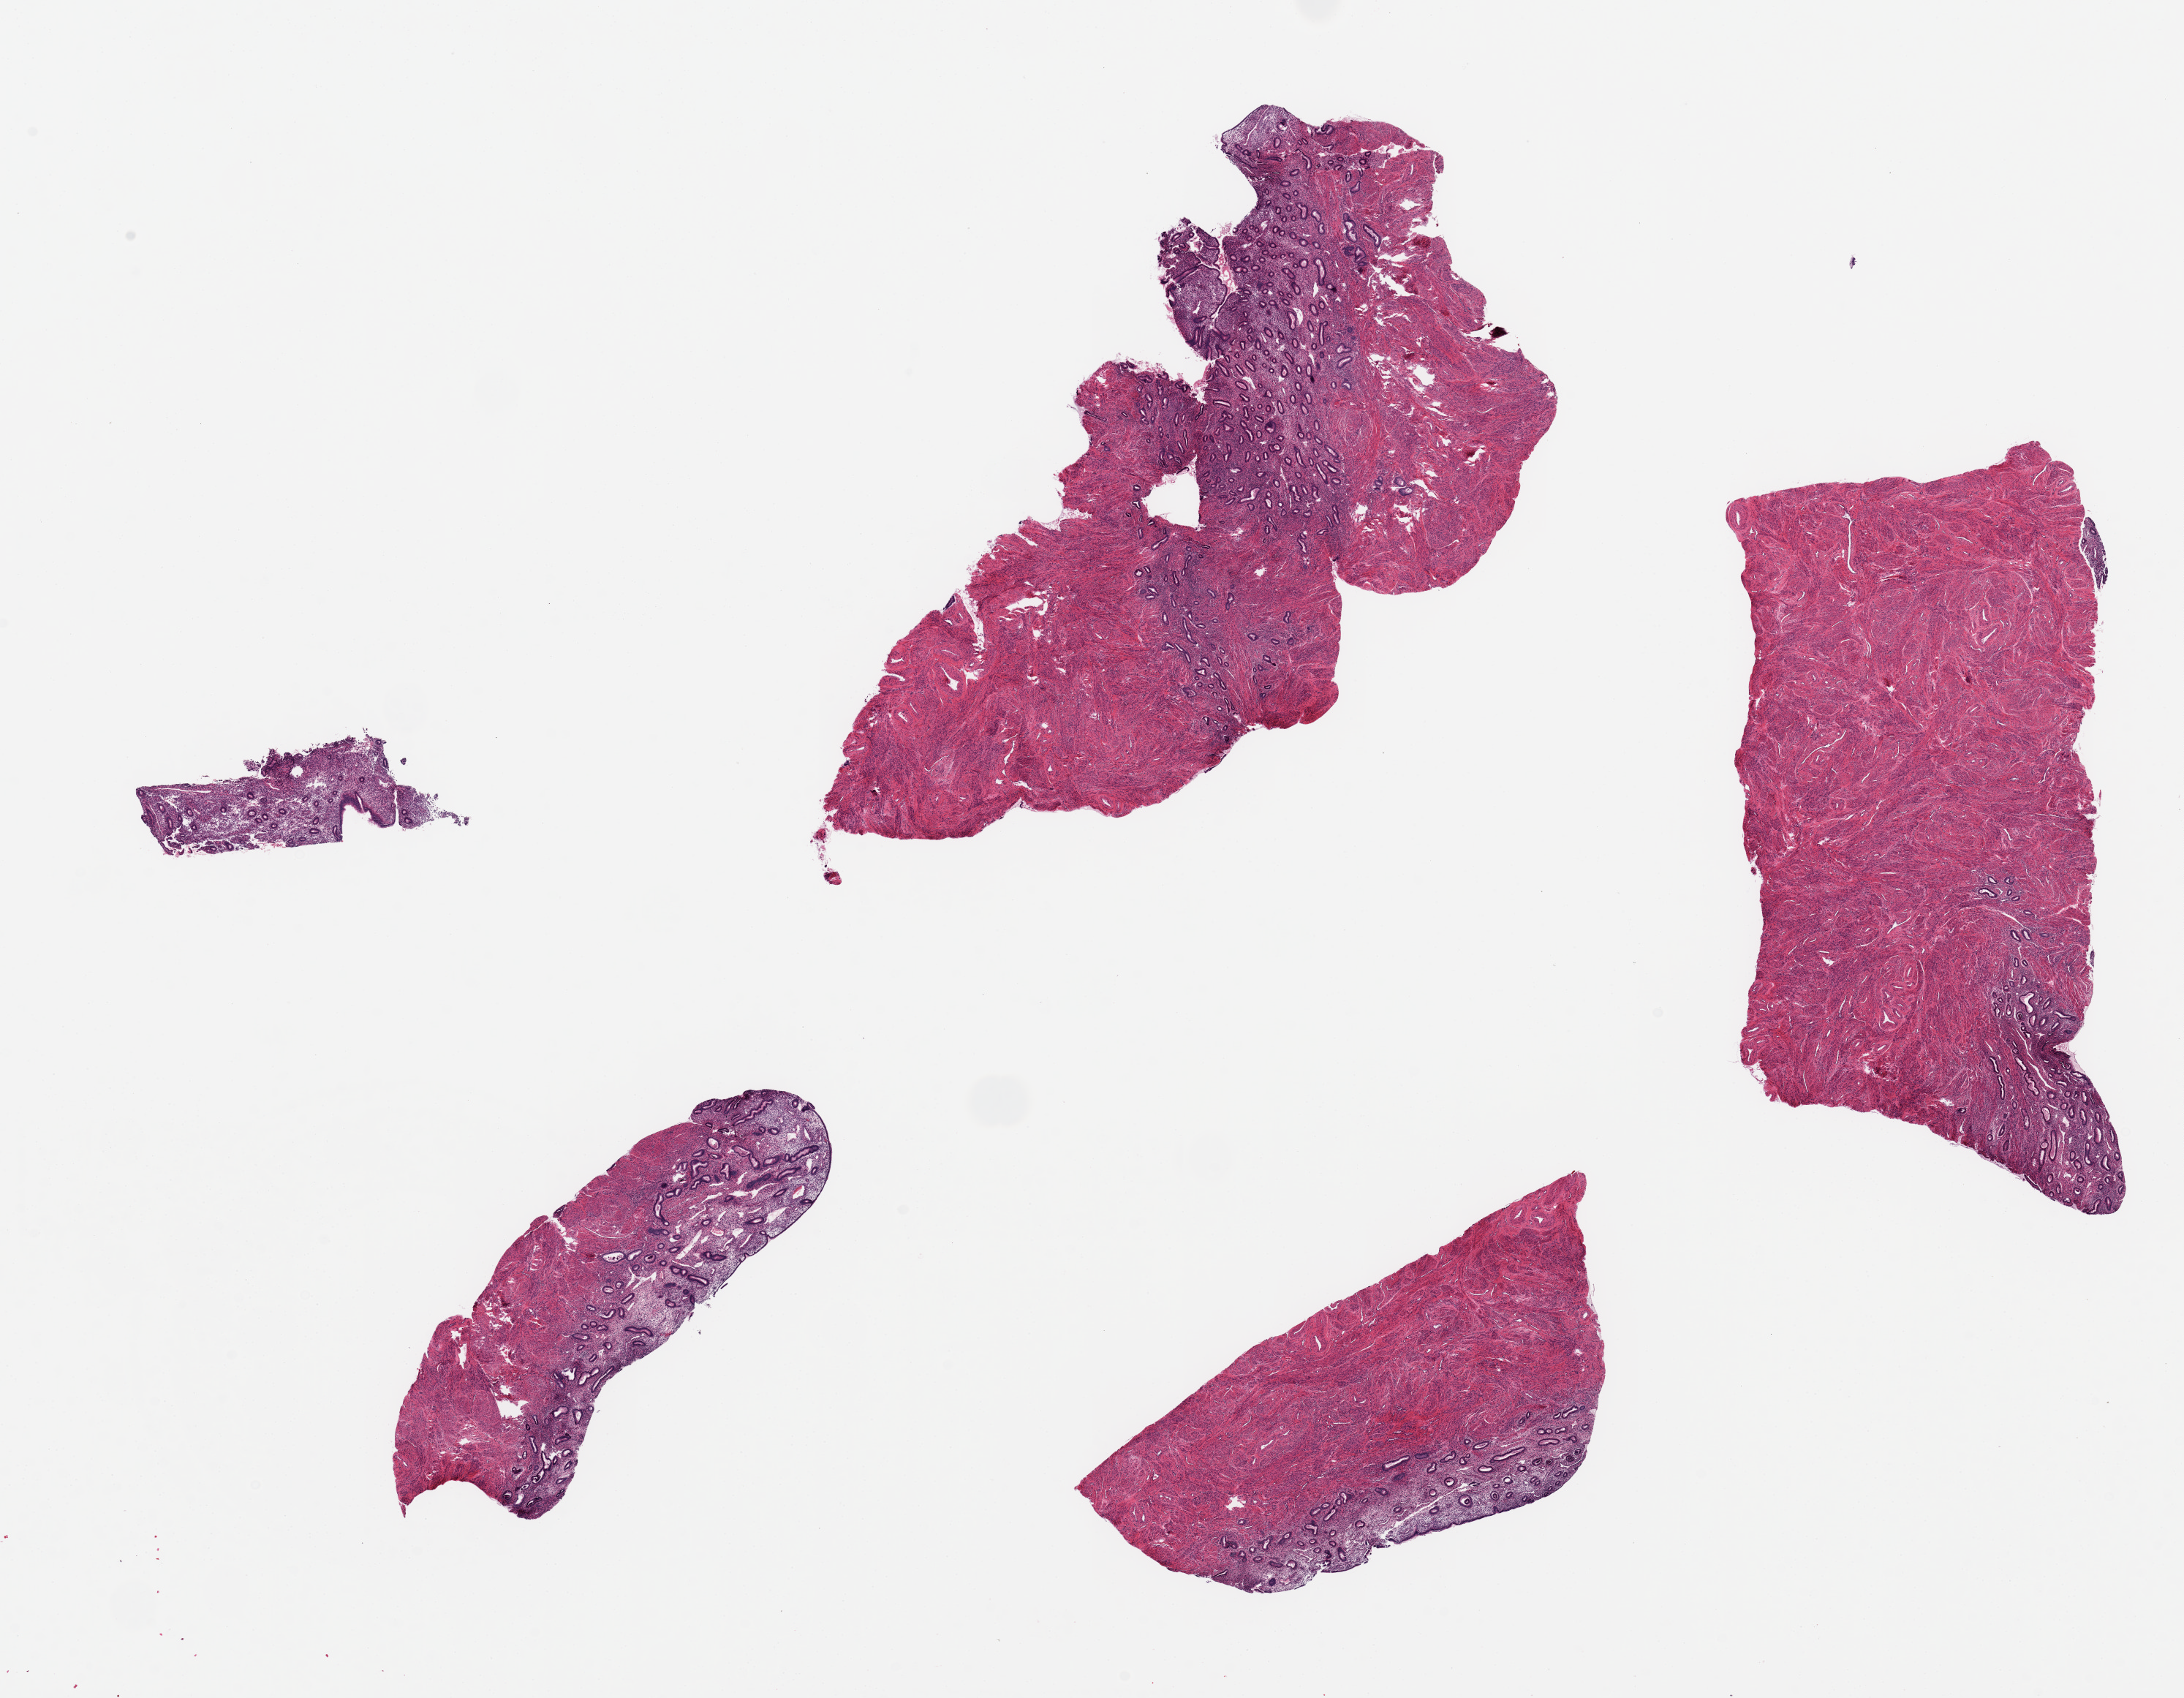
Digitized haematoxylin and eosin-stained section, brightfield — shown as a low-resolution overview of the whole scanned area (about 23.6 x 18.4 mm). PAXgene-fixed paraffin-embedded (PFPE) section. Target tissue: uterus. Tissue donor sample. Female donor.
- reviewer comment on this tissue sample: 5 pieces up to 9x3mm. Not endocervix, lower uterine segment and endometrium. May be retained after re-lableling